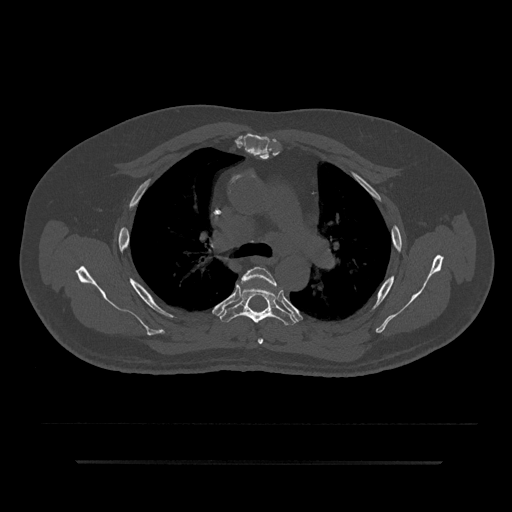
CT including the spine, one axial slice. Reconstruction kernel Br40s/3. Bone window (W 1800 / L 400 HU). 512 × 512 image matrix, field of view 464 × 464 mm. Patient: male, 59 years. From the clinical record (not read from this slice): primary cancer: bile ducts; vertebrae with lytic lesions (as recorded): T10.
Outlined on this slice (semi-automatically segmented with operator editing):
- T4 vertebra: bounding box [x1, y1, x2, y2] px = [241, 266, 277, 344]
- T5 vertebra: [220, 285, 297, 325]